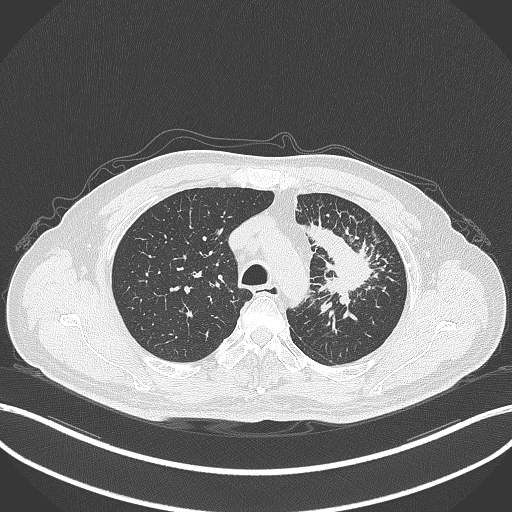
Chest CT, one axial slice; position 271 of 386 along the scan axis; reconstruction kernel B70f; 120 kVp; lung window (W 1500 / L -600 HU); 1 mm slice thickness; 512 × 512 image matrix. Patient: male, 69 years. From the clinical record (not read from this slice): clinical TNM (as recorded): T2a N2 M0; histopathological grade: G2-3.
Outlined on this slice (rectangle marked by the reading radiologist):
- lung tumour (recorded histology: adenocarcinoma): box from (x=301, y=220) to (x=383, y=307) px